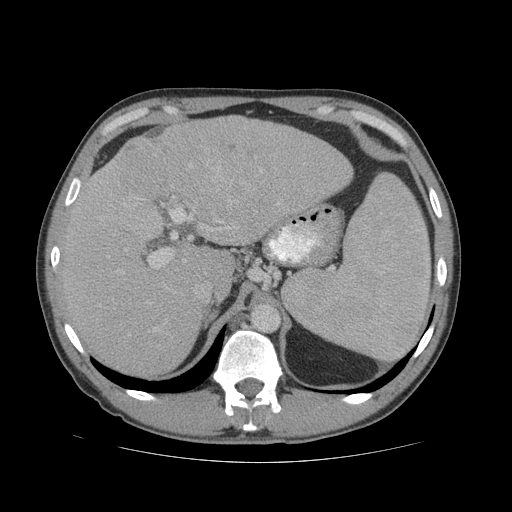
Contrast-enhanced abdominal CT (liver protocol), one axial slice. Soft-tissue window (W 400 / L 40 HU). 512 × 512 image matrix, field of view 400 × 400 mm. From the clinical record (not read from this slice): diagnosis: hepatocellular carcinoma (patient treated with transarterial chemoembolisation; whether this scan precedes or follows treatment is not stated here); TNM stage (as recorded): Stage-IVB; Child-Pugh class: B.
Annotated regions visible in this slice (semi-automatically segmented with operator editing):
- liver parenchyma outside the tumour (the mass and vessels are separate outlines, so this box may not span the whole liver): bounding box (x1, y1, x2, y2) in pixels: (58, 116, 352, 376)
- mass: (111, 124, 214, 202)
- liver vessels: (99, 167, 280, 332)